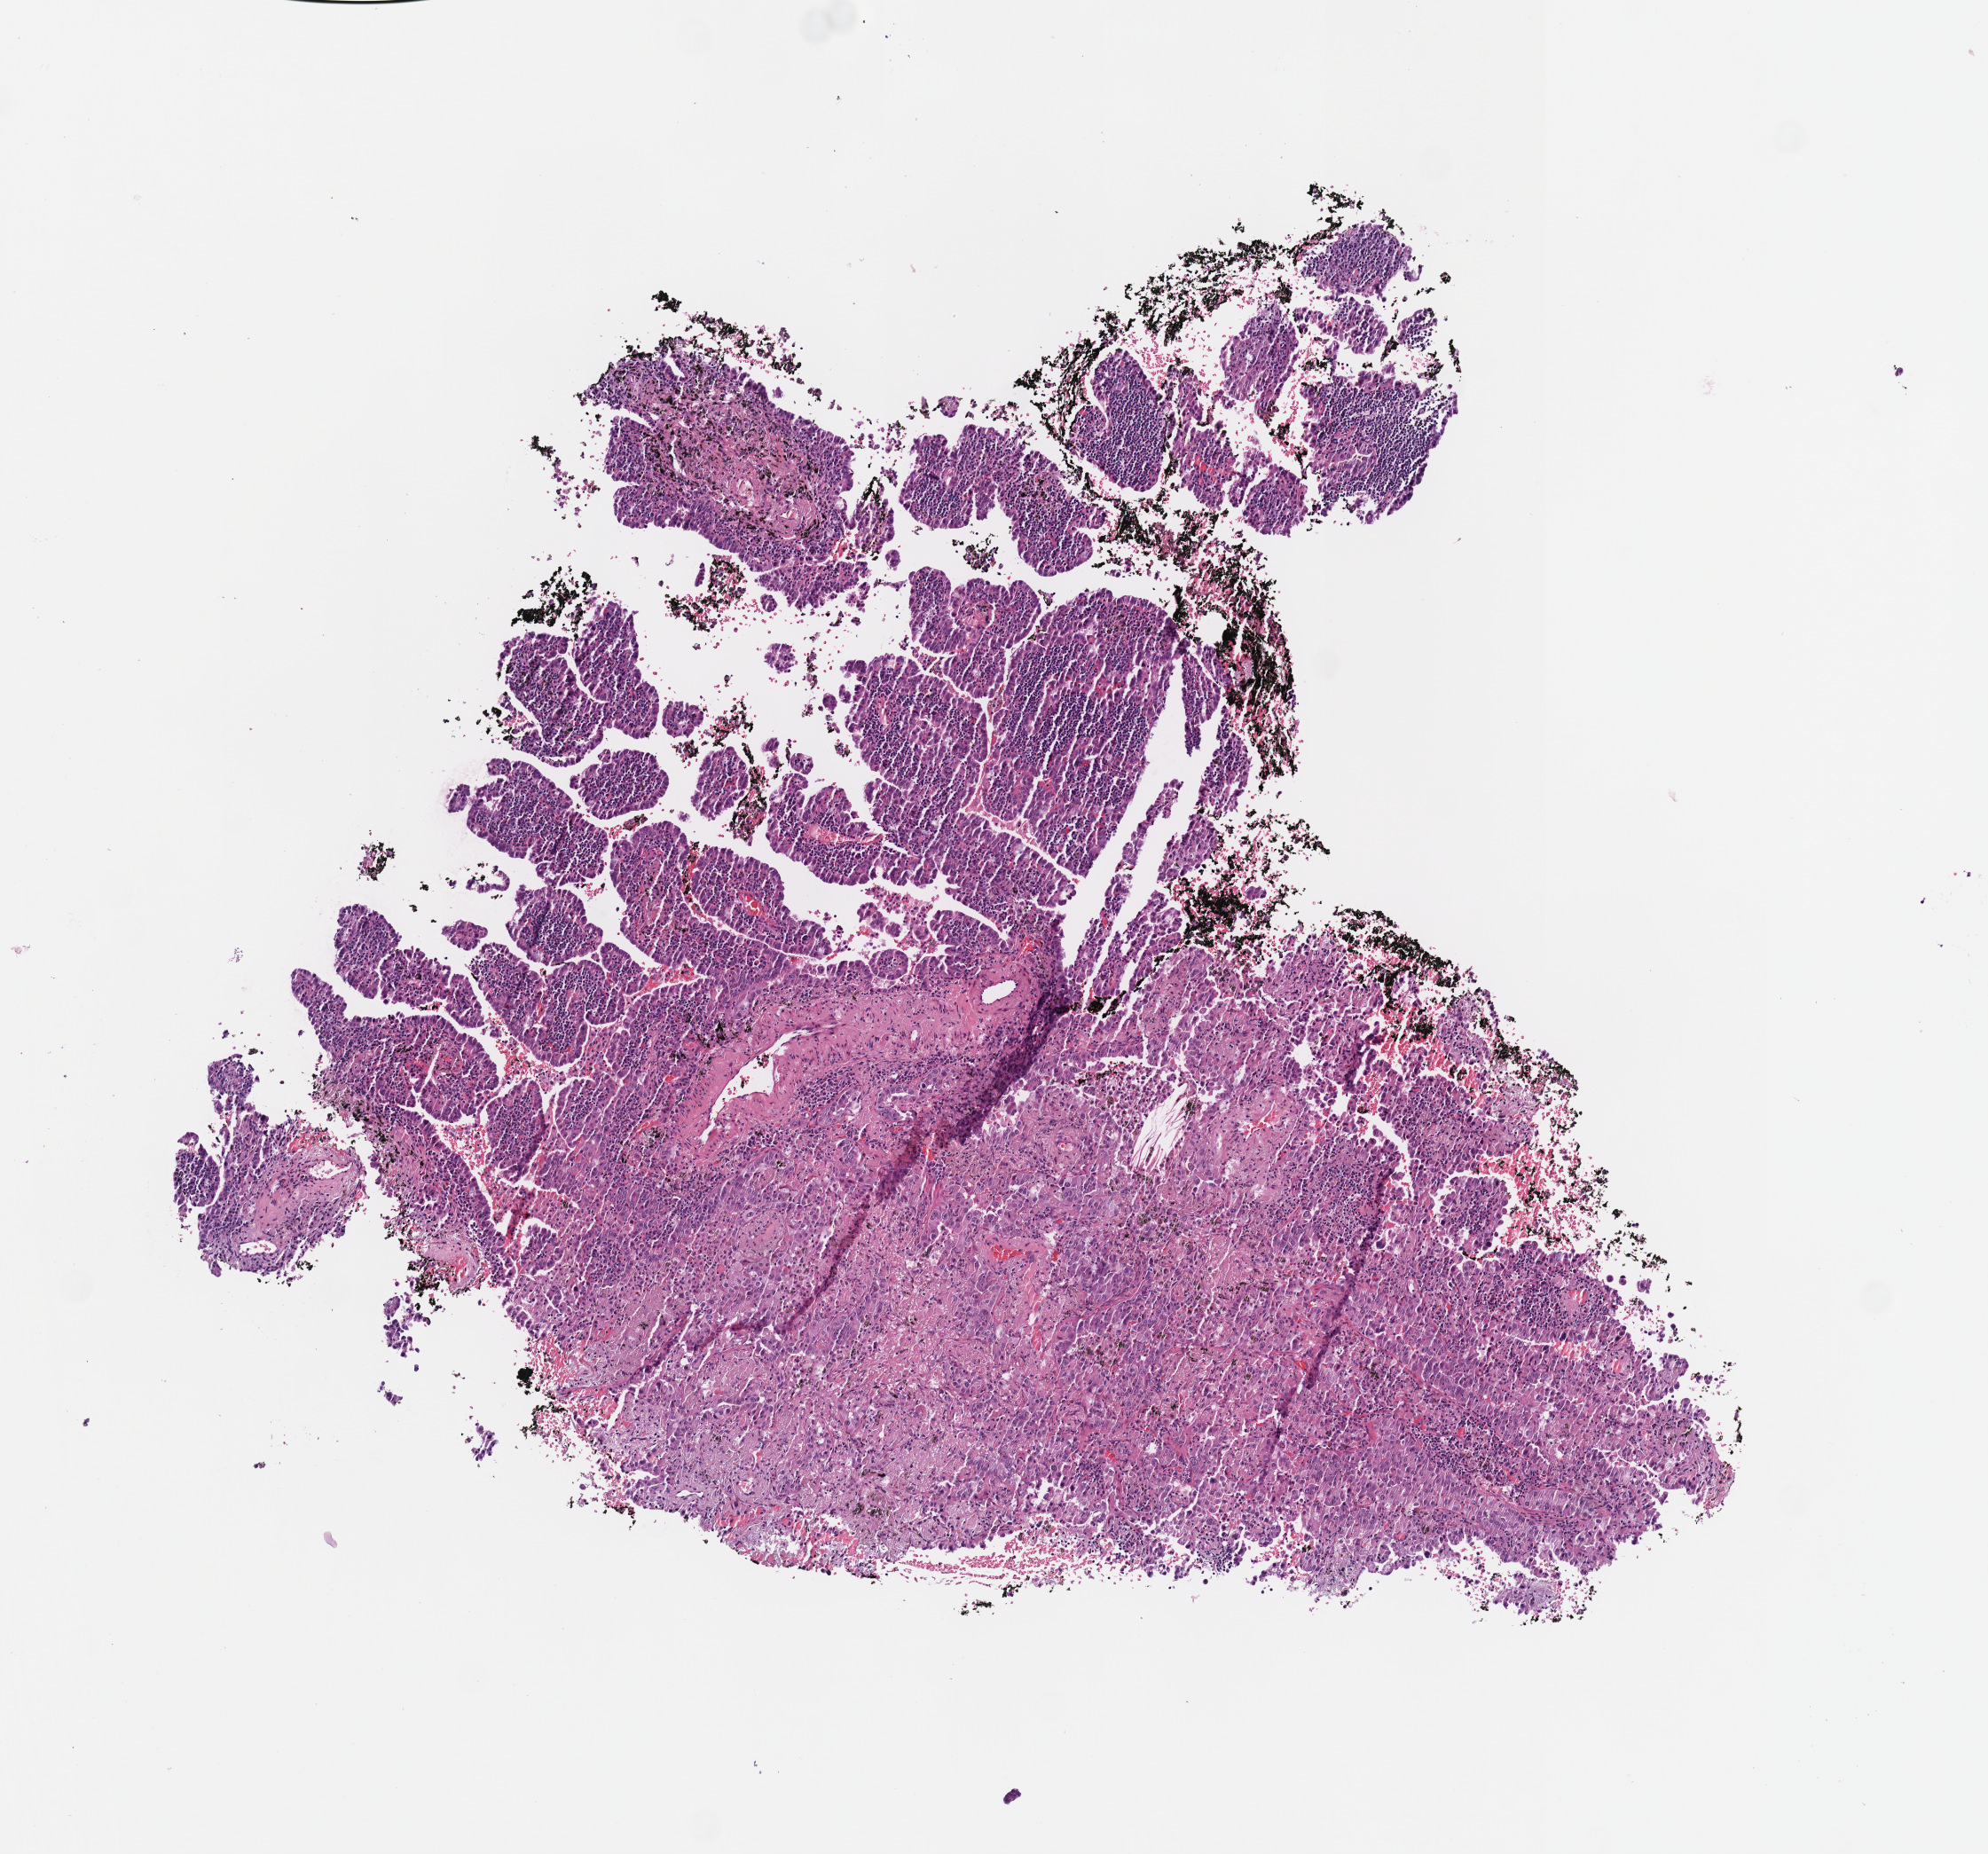
Whole-slide histology image, H&E-stained, low-resolution overview of the scanned area, about 4.4 x 4.1 mm (from a 40x scan); formalin-fixed paraffin-embedded (FFPE) diagnostic section; sample: primary tumour, lung. Male patient; age at initial diagnosis 58 years.
AJCC pathologic stage: IB (7th edition). Histologic diagnosis: Adenocarcinoma, NOS (lower lobe, lung).